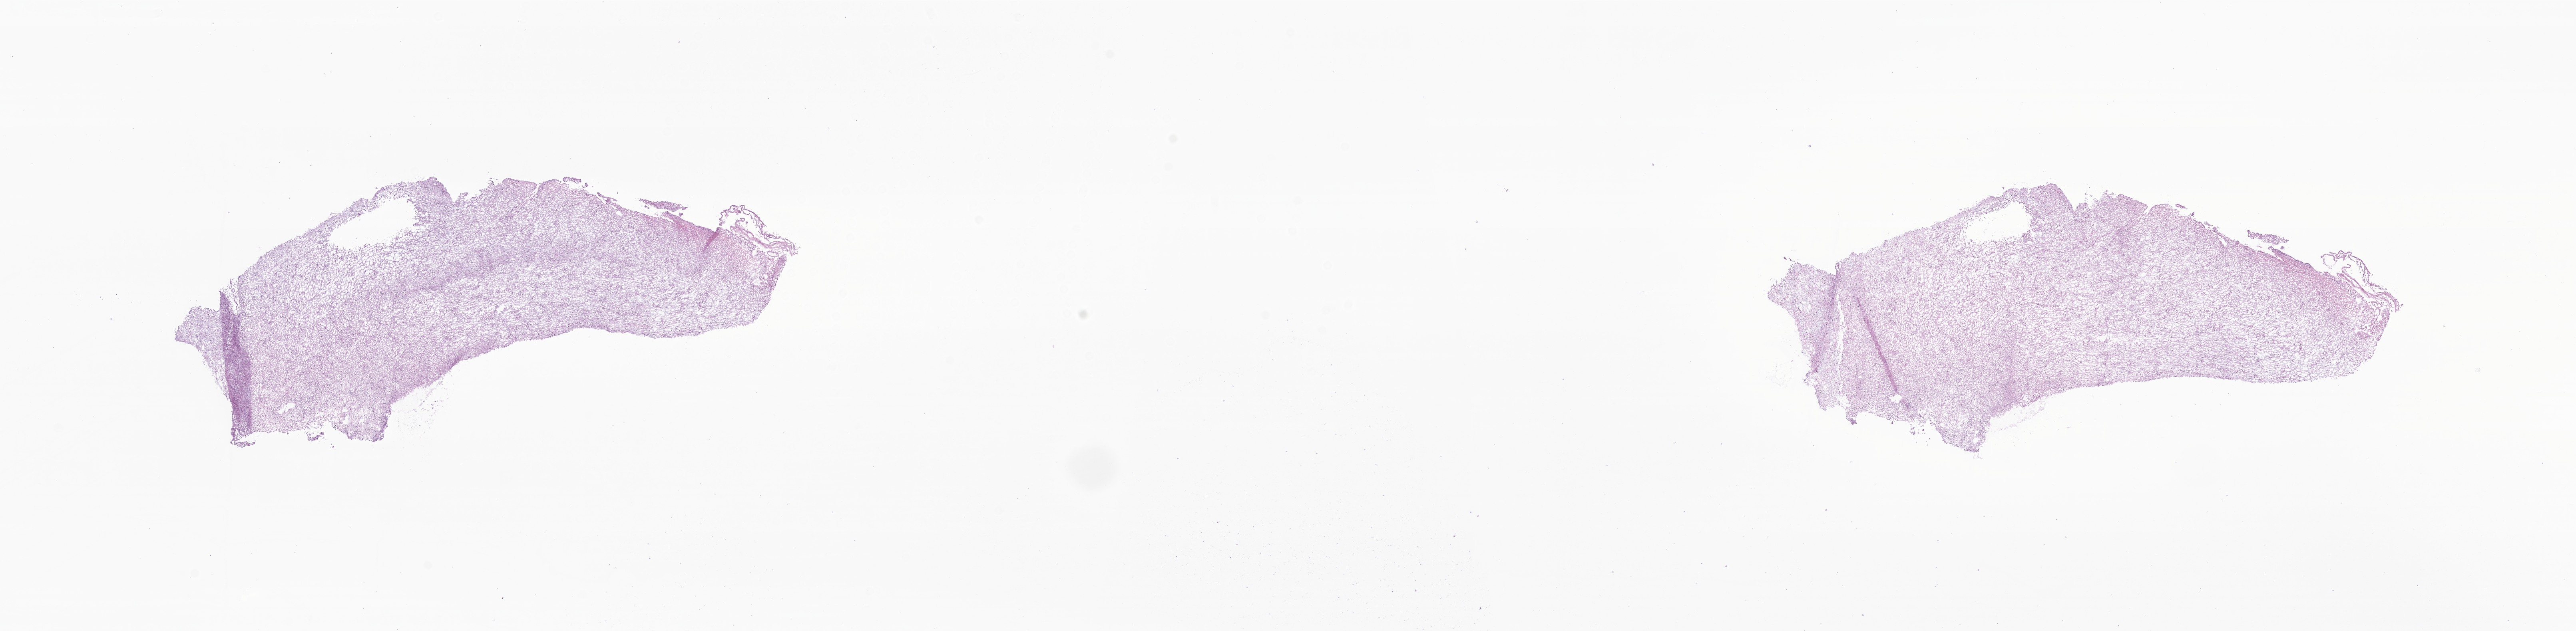
Whole-slide image, H&E stain of tumor tissue from the brain — shown as a low-resolution overview of the whole scanned area (about 27.2 x 6.7 mm). Frozen section. Female patient, age 185 months (15 years 5 months).
Diagnosis (ICD-O-3 morphology term): Astrocytoma, NOS.